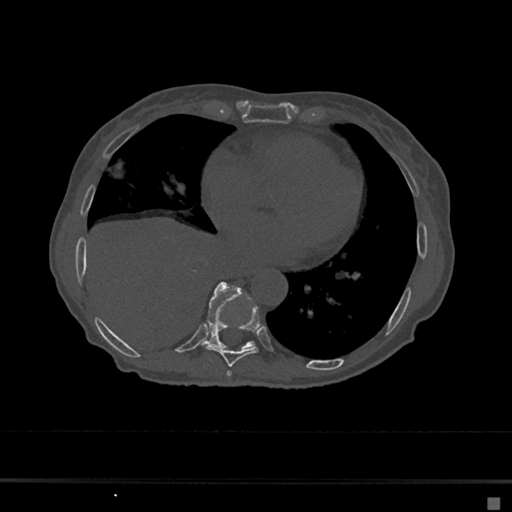
CT including the spine, one axial slice. Slice 304 of 797 in the series (ordered by position). 120 kVp. Bone window (W 1800 / L 400 HU). 0.5 mm slice thickness. 512 × 512 image matrix, field of view 360 × 360 mm. Patient: female, 68 years. Case-level facts recorded for this patient, not image findings: primary cancer: renal.
Outlined on this slice (semi-automatic segmentation, software-assisted and operator-edited):
- T7 vertebra: box from (x=227, y=371) to (x=232, y=377) px
- T8 vertebra: (x=205, y=305)–(x=260, y=367)
- T9 vertebra: (x=206, y=282)–(x=255, y=349)